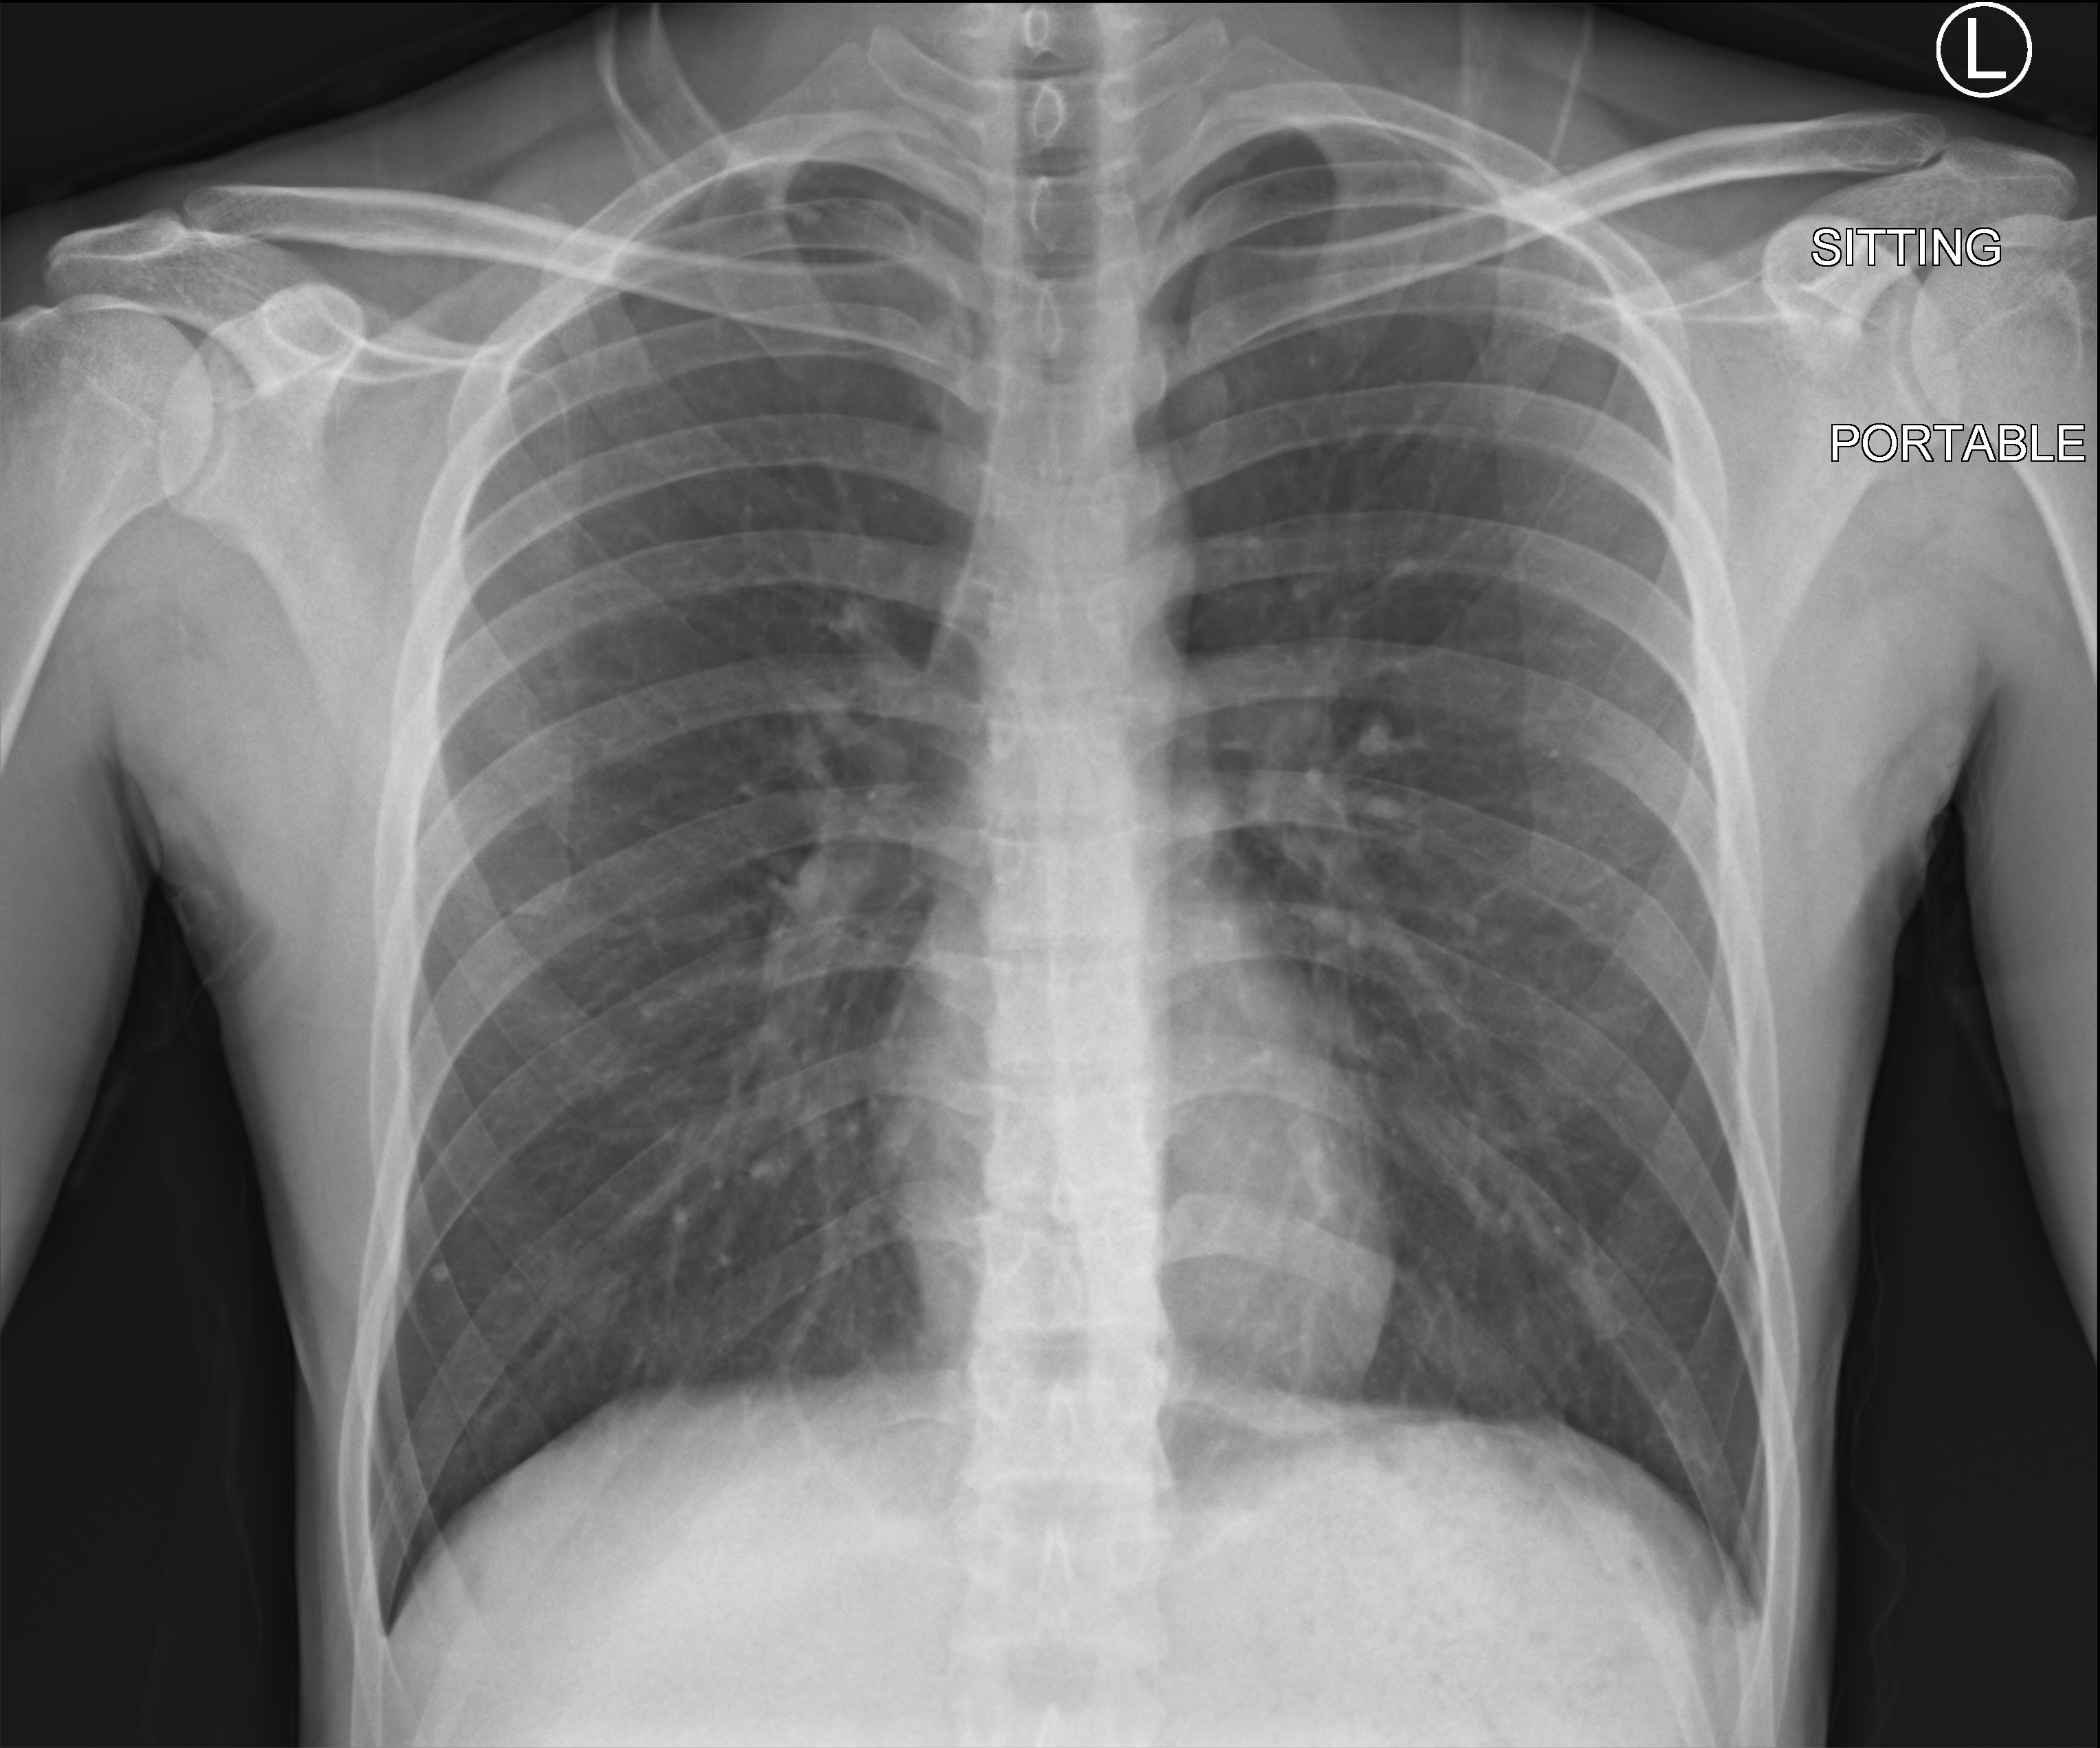
Chest X-ray (portable); anteroposterior (AP) projection. Patient hospitalised with COVID-19; male, aged 18–59 years.
From the hospital-stay record, not from the radiograph (when in the stay this image was taken is not recorded):
- other chronic lung disease (admission record): no
- mechanically ventilated during this hospital stay: no